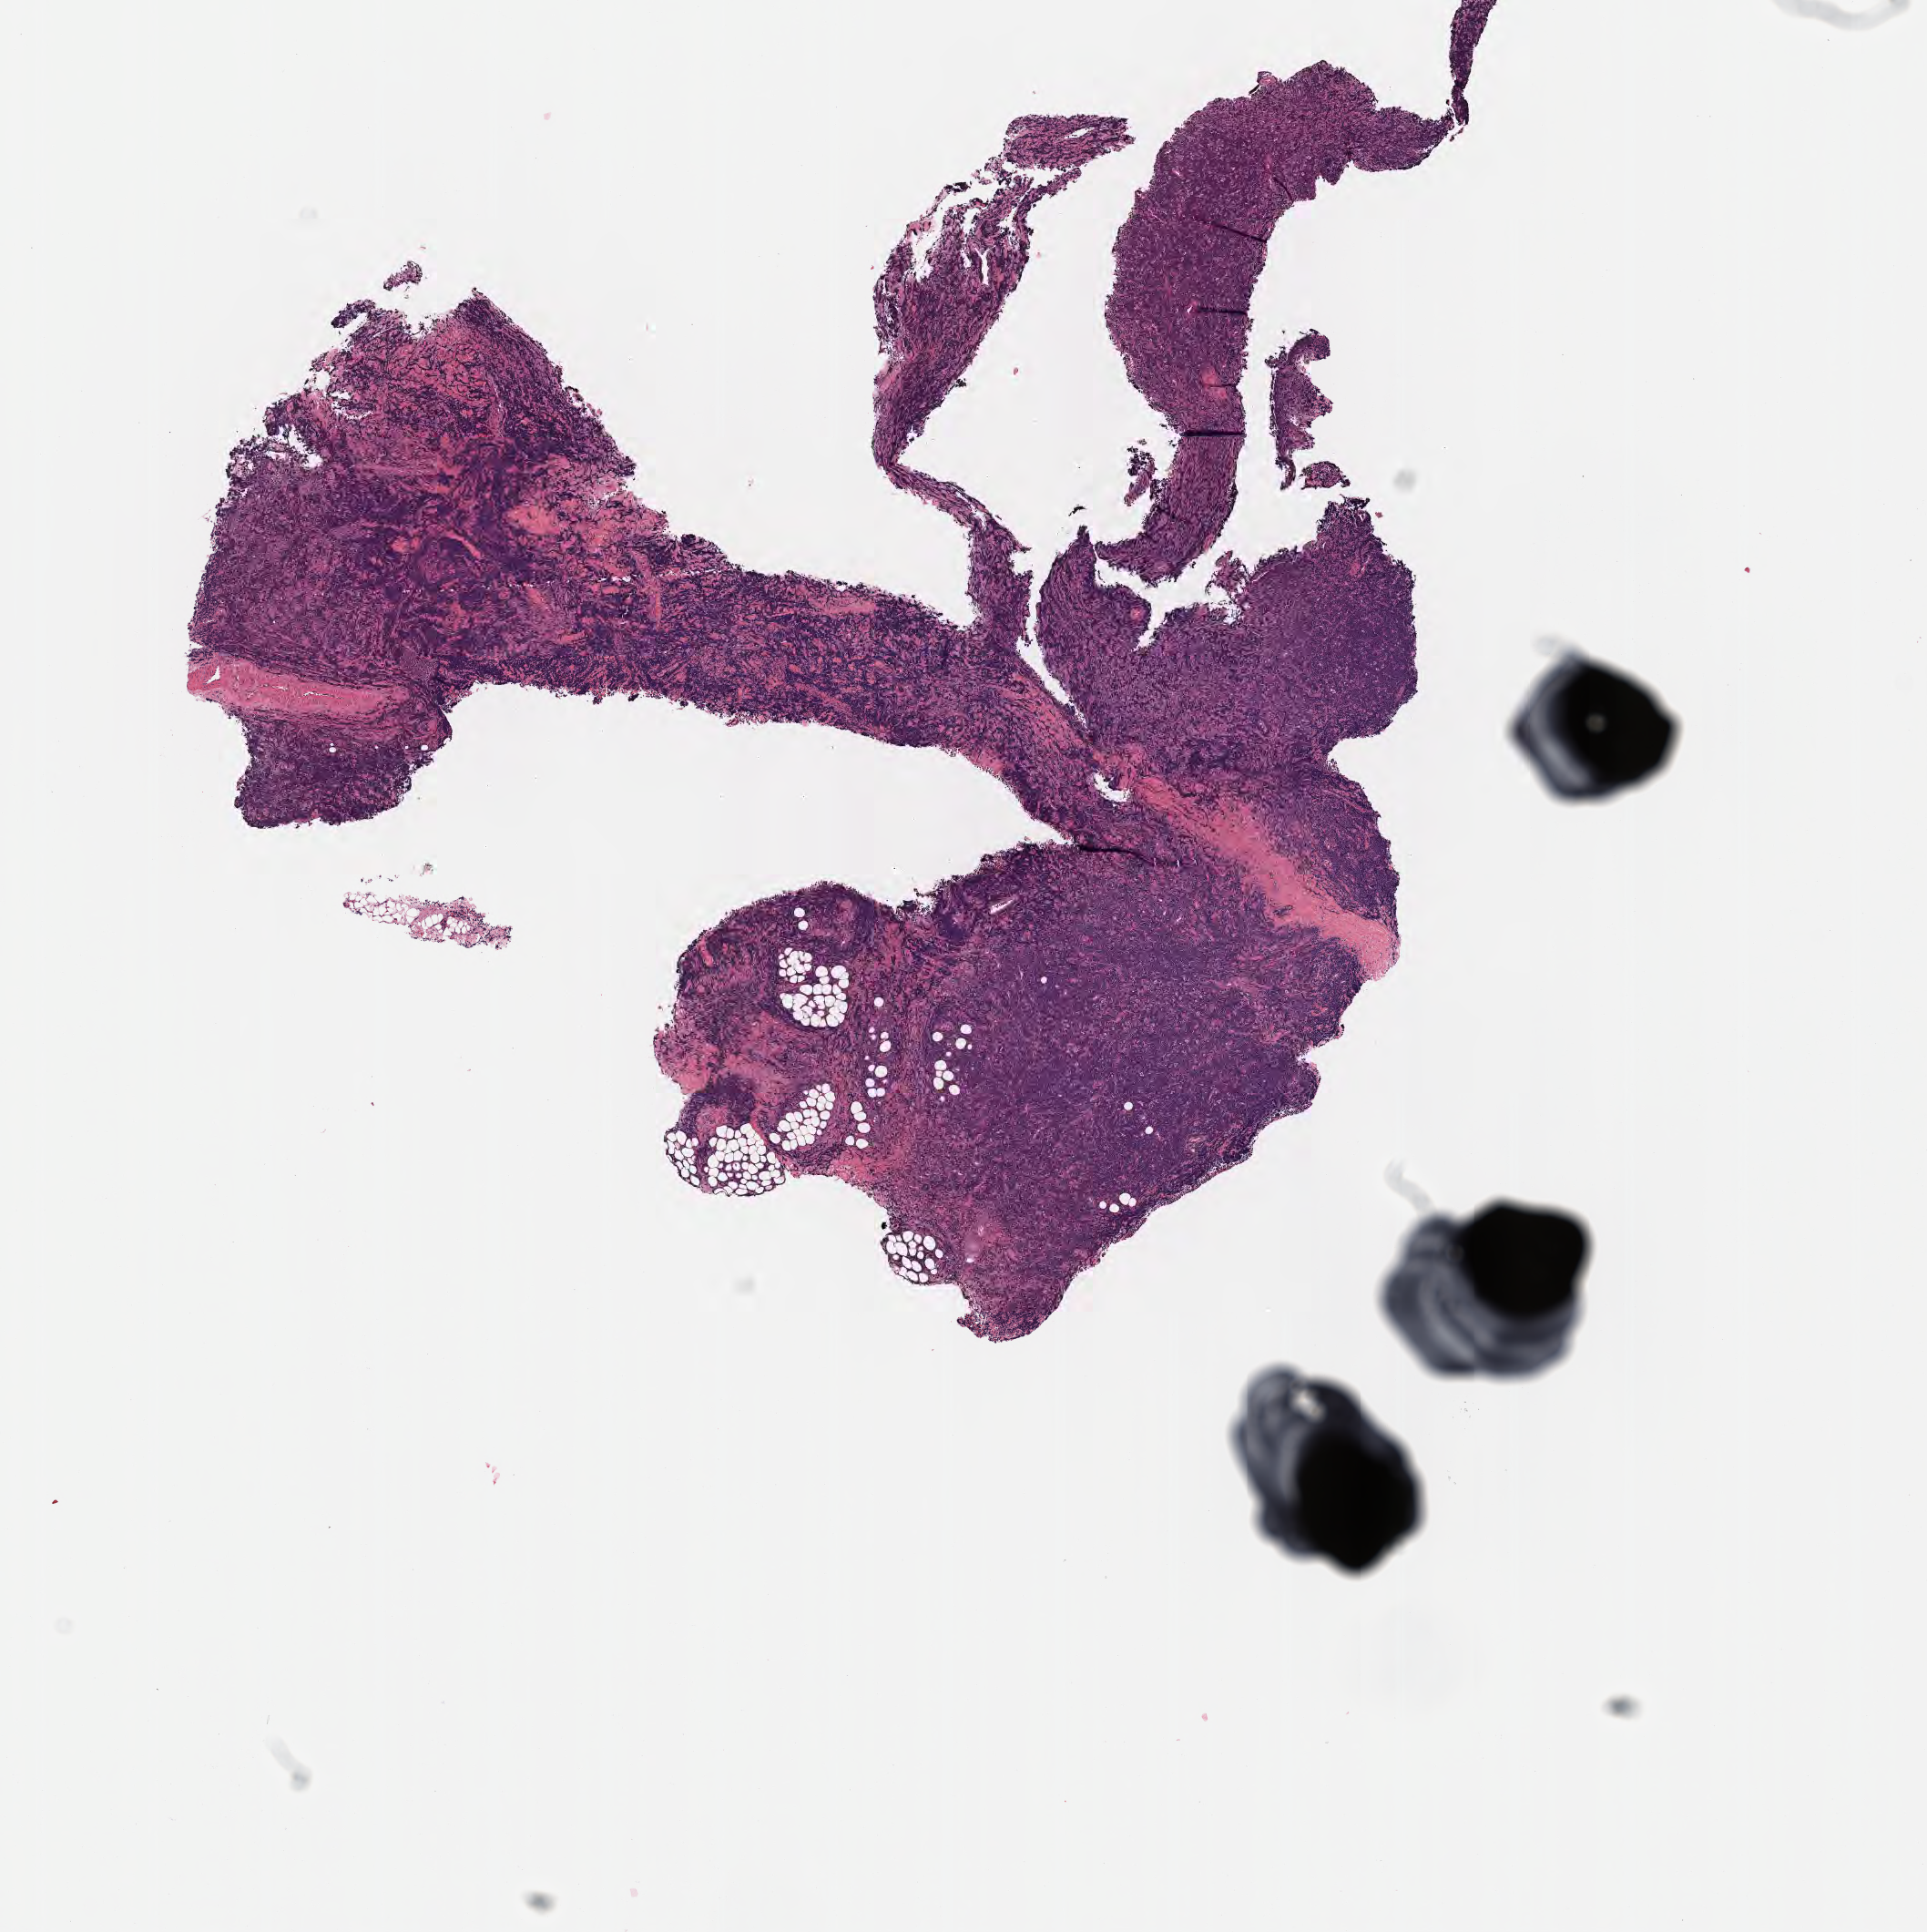
Hematoxylin and eosin (H&E) whole-slide image, shown as a low-resolution overview of the whole scanned area (about 8.6 x 8.6 mm); specimen: tumor tissue; site: cranium. Male patient; age at initial diagnosis 2 years.
Diagnosis: Burkitt lymphoma, NOS.